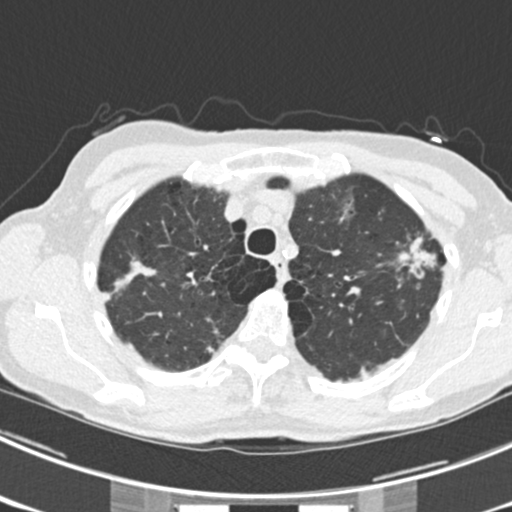
Chest CT (low-dose screening protocol), one axial image. Third screening round (two years after baseline). Lung window (W 1500 / L -600 HU). 2 mm slice thickness. 120 kVp. 512 × 512 image matrix. Female participant, aged 63 years at enrolment.
Lesion marked by an expert reader, box from (x=377, y=225) to (x=449, y=286) px. The screening reader recorded 9 non-calcified nodules or masses ≥4 mm on this exam (left upper lobe, right upper lobe, left upper lobe, left lower lobe, right middle lobe, left lower lobe, left lower lobe, right lower lobe, right lower lobe); which of them this box marks is not recorded. Official screen result: positive, other. Lung cancer was diagnosed 15 days after this screen: bronchiolo-alveolar adenocarcinoma, NOS, right upper lobe, right middle lobe, right lower lobe, left upper lobe, left lower lobe, moderately differentiated (G2), stage IV (AJCC 6th edition).